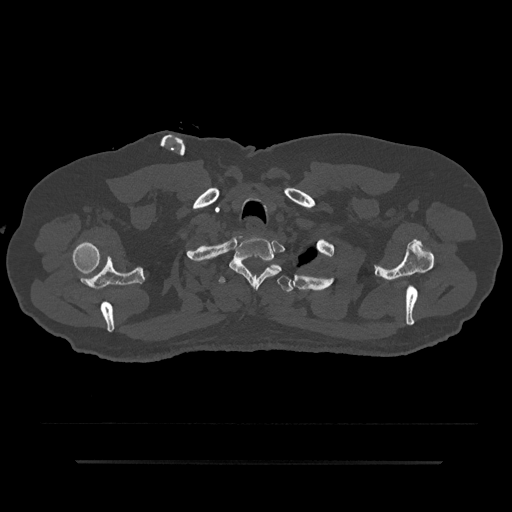
CT including the spine, one axial slice; position 728 of 797 along the scan axis; reconstruction kernel Br40s/3; bone window (W 1800 / L 400 HU); 0.5 mm slice thickness; 512 × 512 image matrix, field of view 464 × 464 mm. Male patient, age 59 years. From the clinical record (not read from this slice): primary cancer: bile ducts; vertebrae with lytic lesions (as recorded): T10.
Structures marked on this image (semi-automatically segmented with operator editing):
- T1 vertebra: box from (x=229, y=236) to (x=282, y=289) px
- T2 vertebra: (x=218, y=264)–(x=293, y=292)